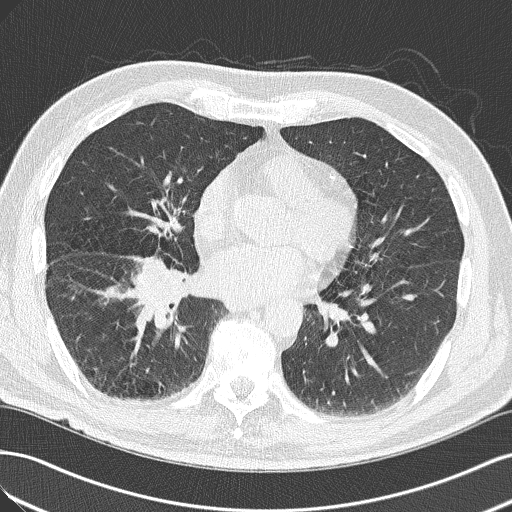
Low-dose screening chest CT, axial slice, first (baseline) screen, lung window (W 1500 / L -600 HU), 2 mm slice thickness, lung (sharp) reconstruction kernel (B50f), slice 89 of 143 in the series. Male participant, aged 65 years at enrolment. Current smoker at enrolment.
- Expert reader's lesion annotation, box from (x=103, y=250) to (x=205, y=340) px.
- The exam's reader record, not a measurement of the box and not confirmed to be the same lesion: non-calcified nodule or mass ≥4 mm, right upper lobe, 18 × 13 mm, spiculated (stellate) margins, soft tissue attenuation.
- Official screen result: positive, change unspecified: nodule(s) >= 4 mm or enlarging nodule(s), mass(es), or other non-specific abnormalities suspicious for lung cancer.
- Lung cancer was diagnosed 14 days after this screen: adenocarcinoma, NOS, right lower lobe, poorly differentiated (G3), stage IIIA (AJCC 6th edition), 40 mm at pathology.